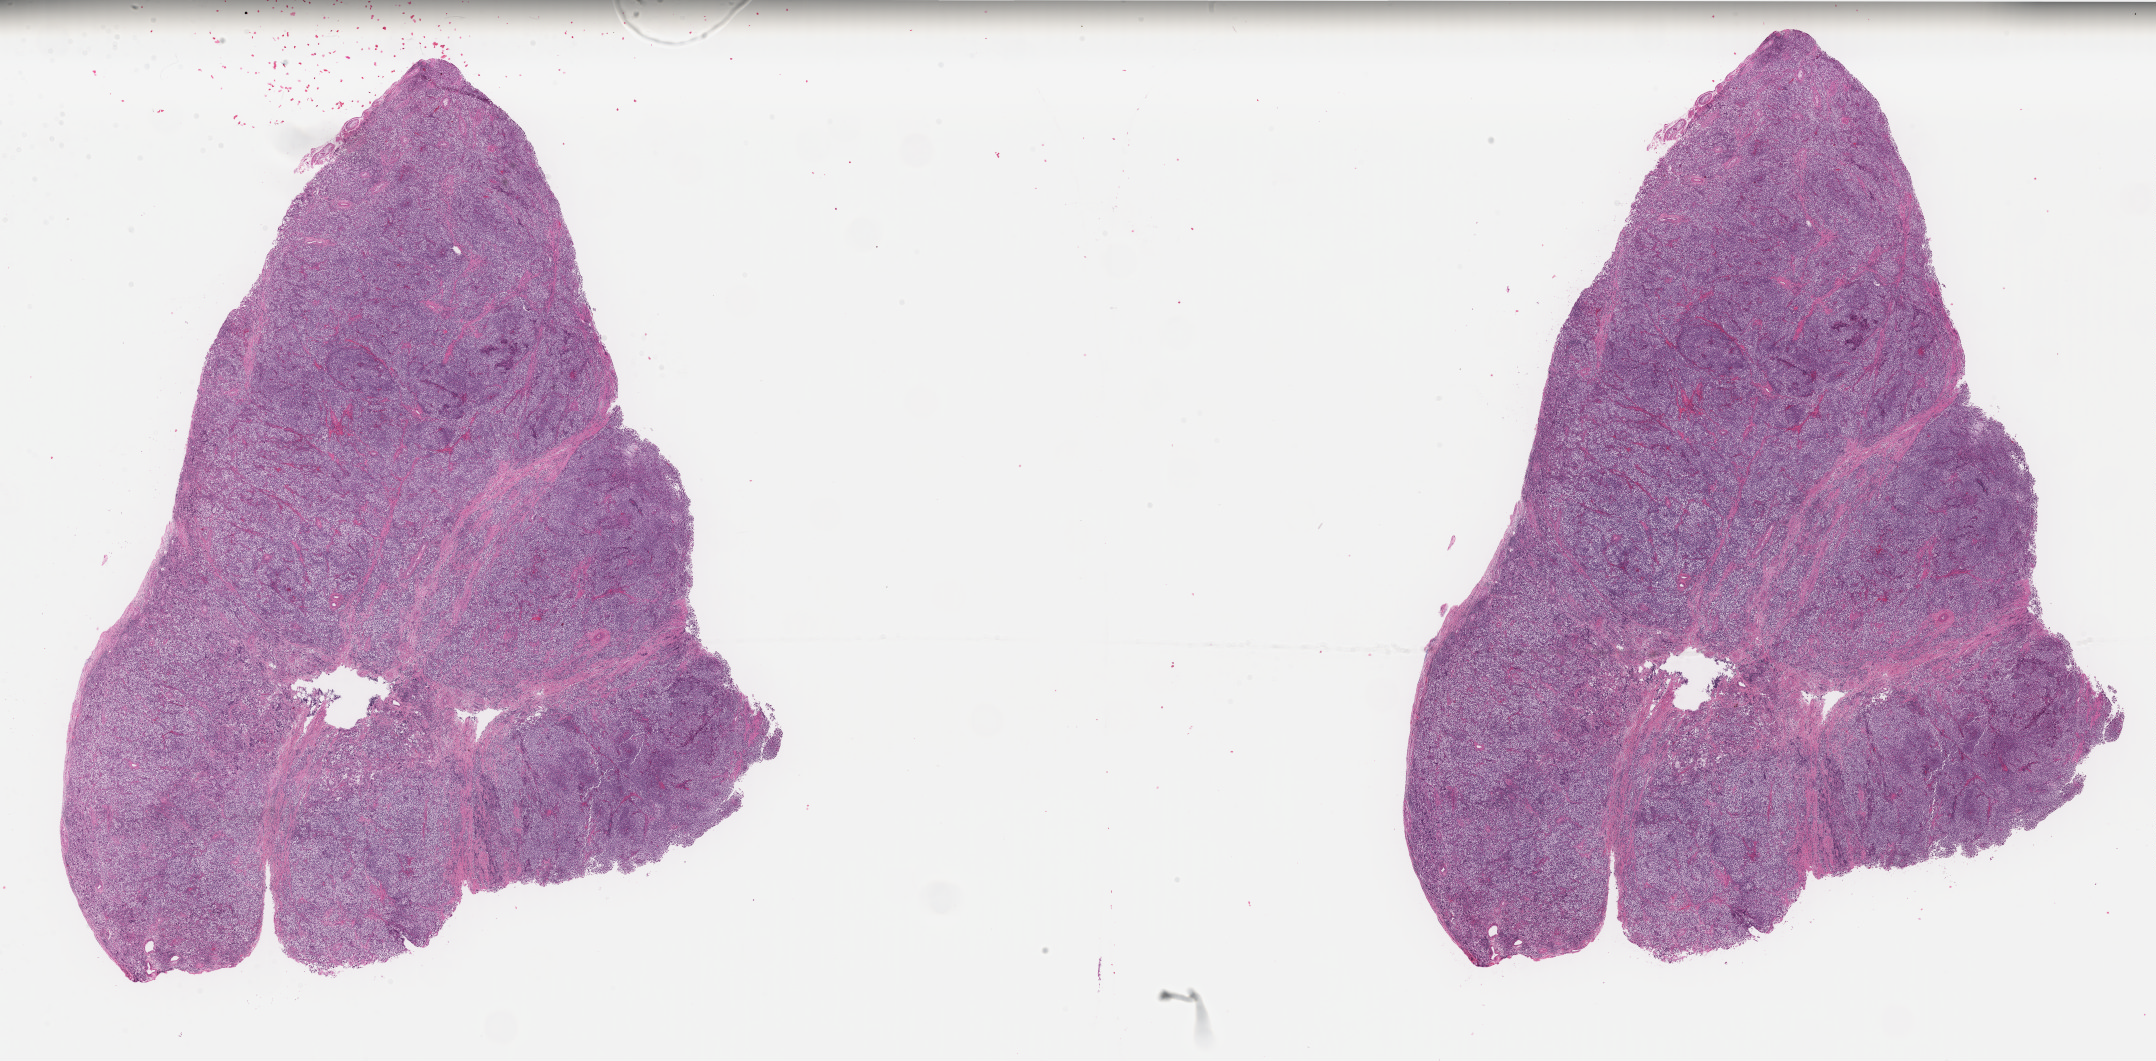
Digitized Hematoxylin and eosin (H&E) stained tissue section (whole slide) — shown as a low-resolution overview of the whole scanned area (about 34.1 x 16.8 mm, slide scanned at 40x). Formalin-fixed paraffin-embedded (FFPE) diagnostic section. Primary tumour sample from the testis. Patient: male, age at initial diagnosis 26 years.
Histologic diagnosis: Mixed germ cell tumor. Laterality: left.